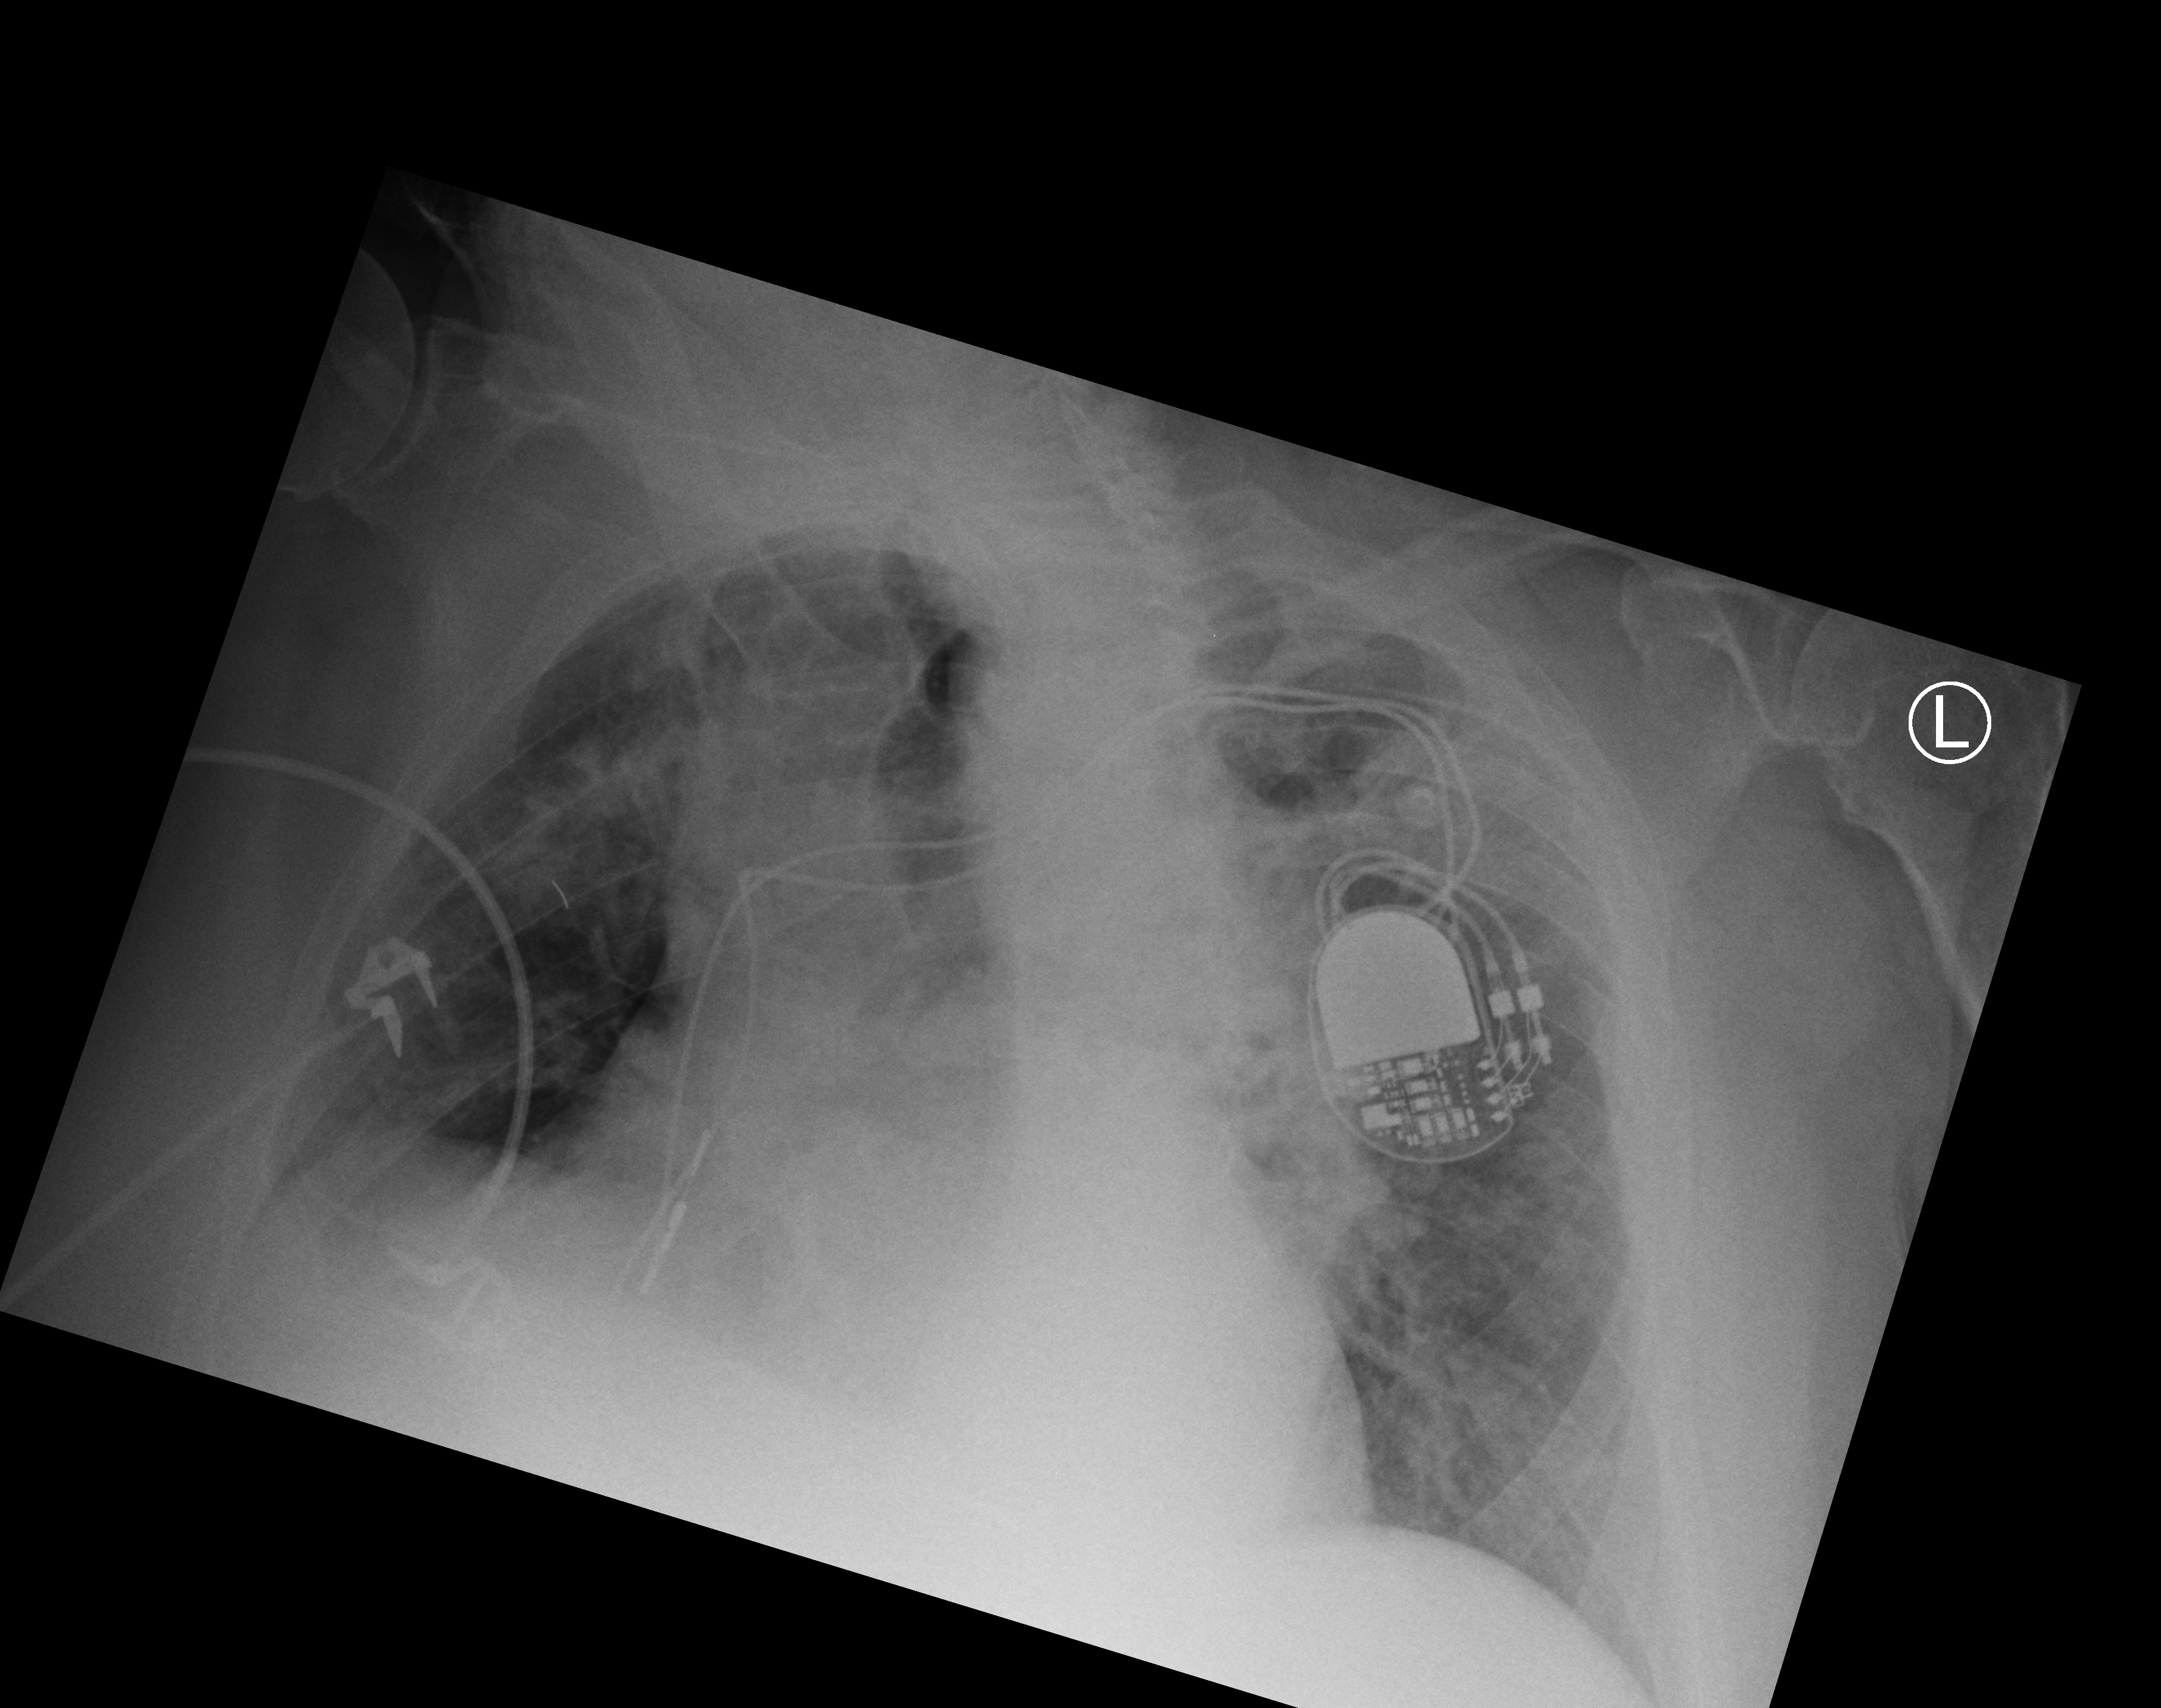
Portable chest radiograph, anteroposterior (AP) projection. Patient hospitalised with COVID-19; male, aged 75–90 years.
Hospital-stay facts (about this admission, not read from this image; timing relative to this image not recorded): mechanically ventilated during this hospital stay: no; admitted to intensive care during this hospital stay: no; hypertension (admission record): yes.